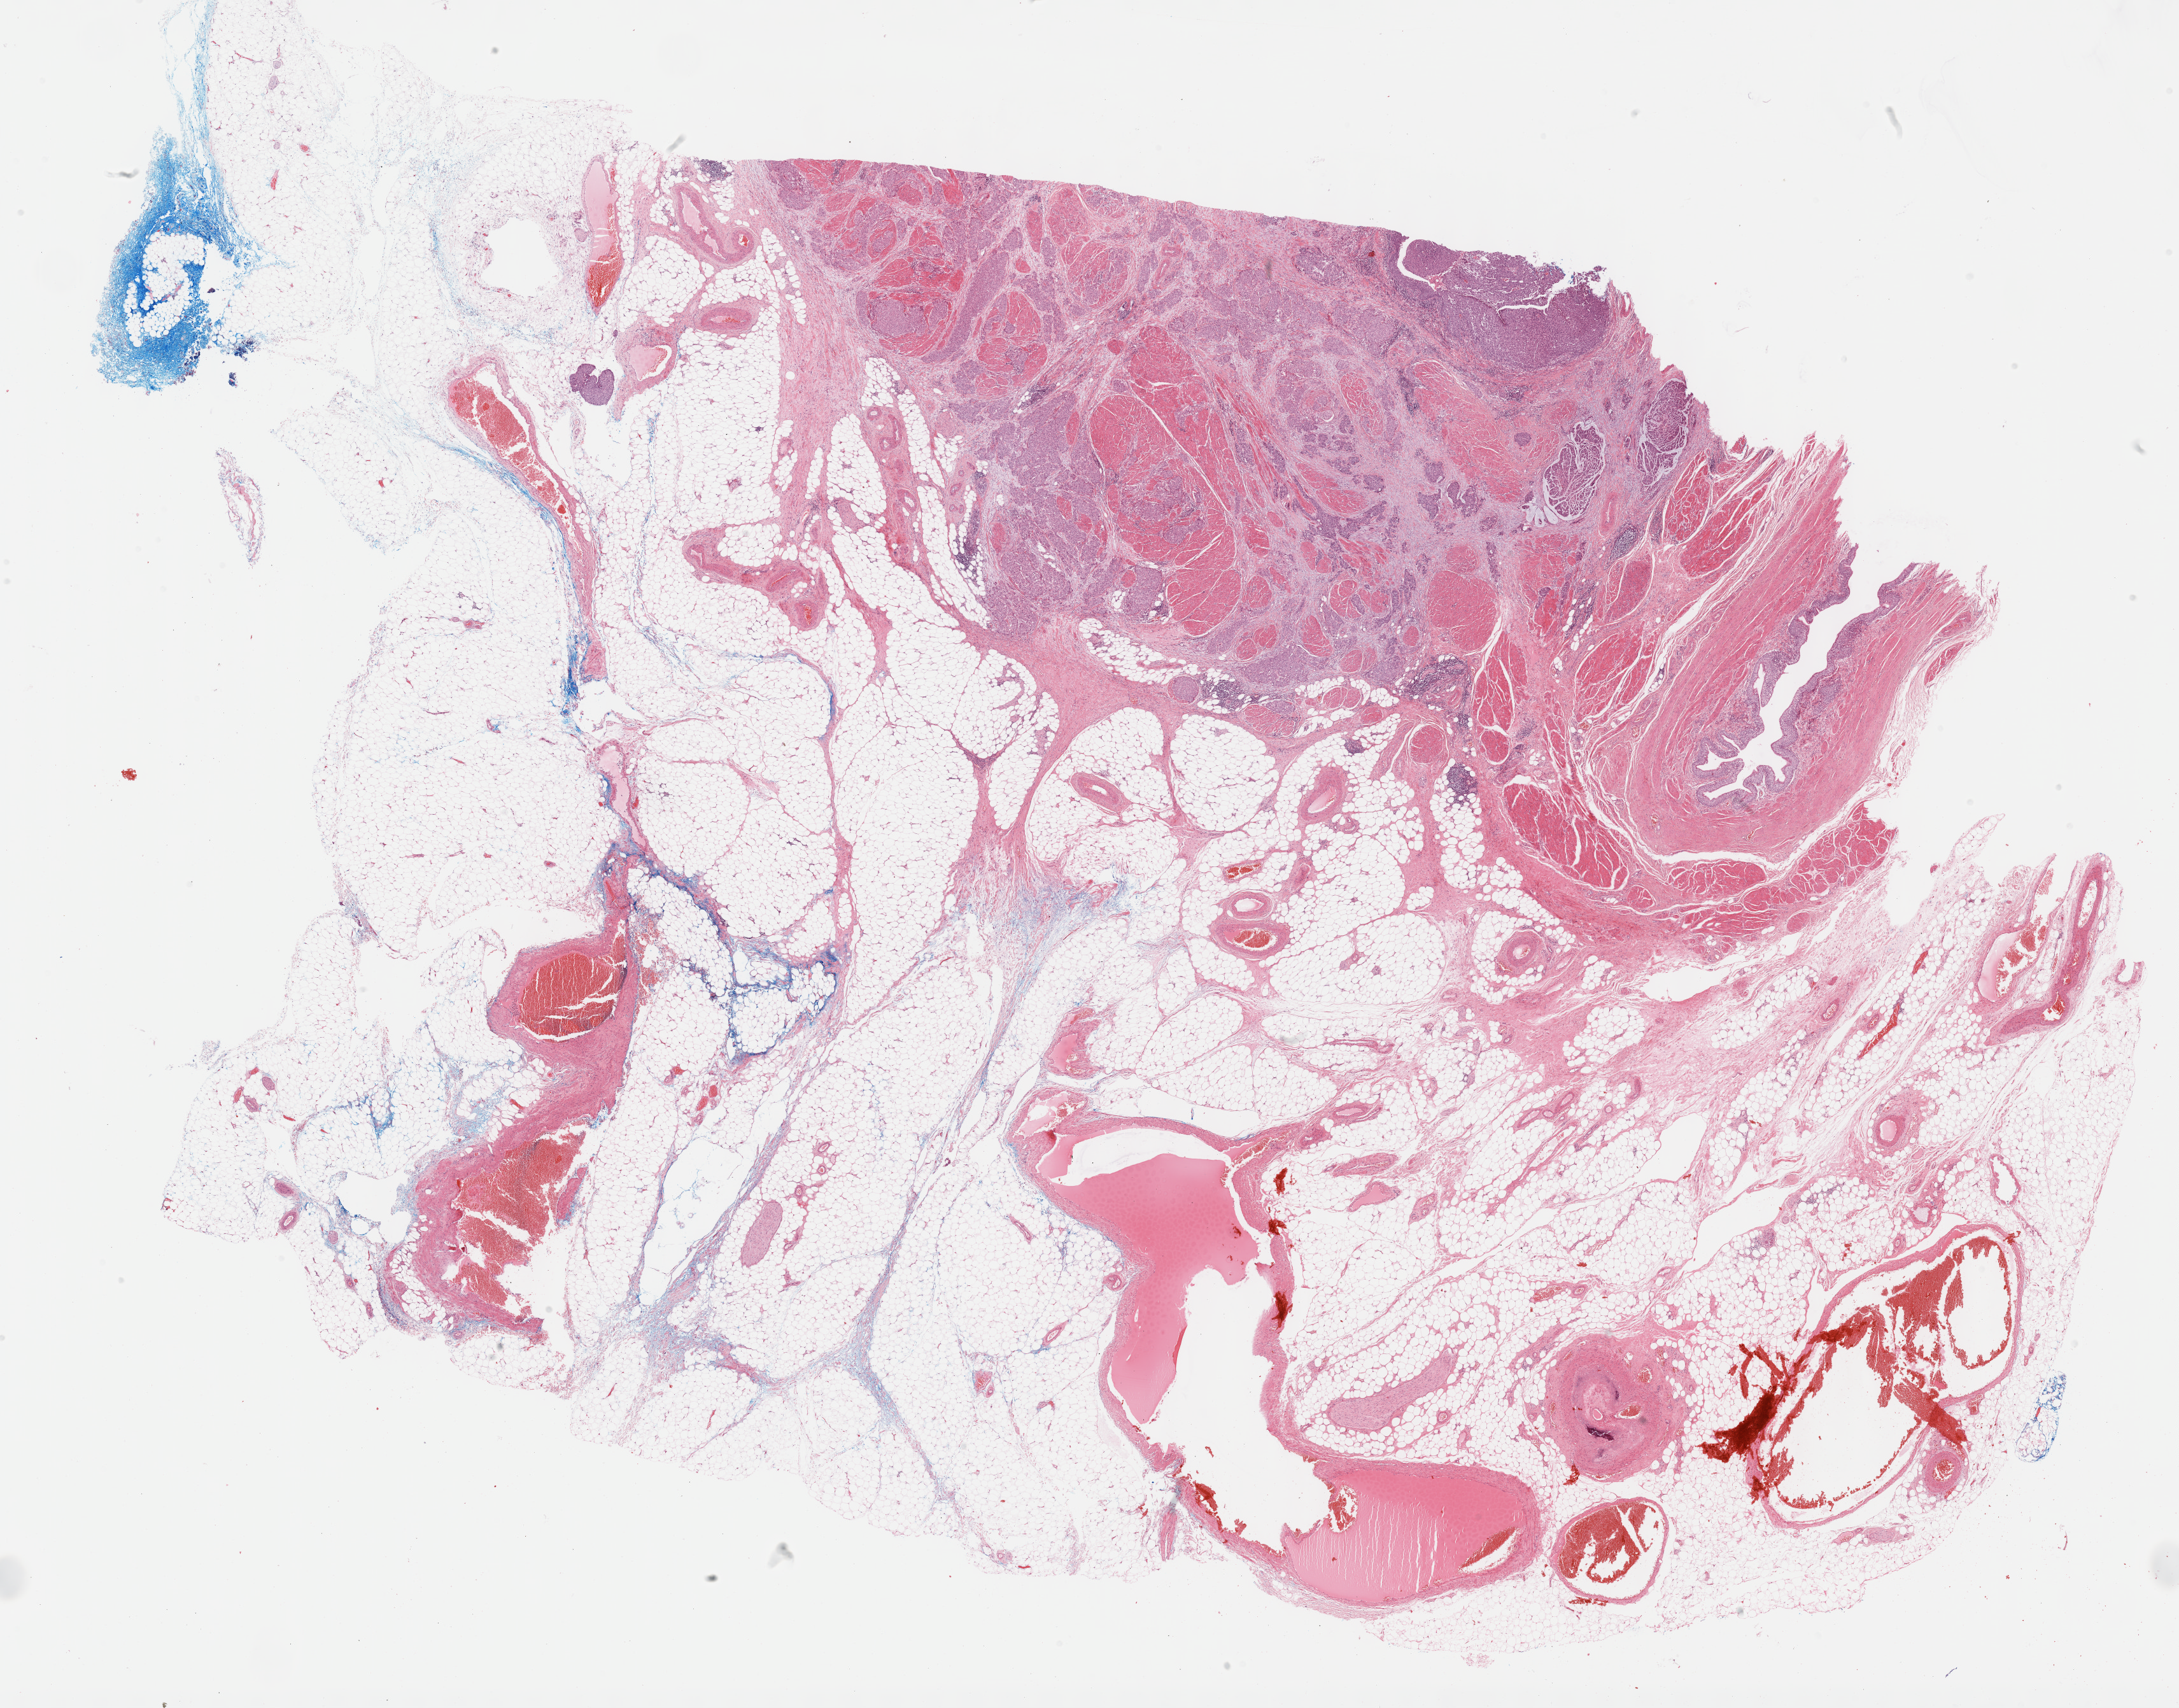
Digitized Hematoxylin and eosin (H&E) stained tissue section (whole slide), whole scanned area (about 27.7 x 21.7 mm, from a 40x scan) shown as a low-resolution overview. Formalin-fixed paraffin-embedded (FFPE) diagnostic section. Primary tumour sample from the bladder. Male, age 81 years at initial diagnosis. Histologic grade: high grade.
Histologic diagnosis: Transitional cell carcinoma. AJCC pathologic stage: IV (7th edition). Lymph nodes positive (case pathology): 2 of 13 examined.